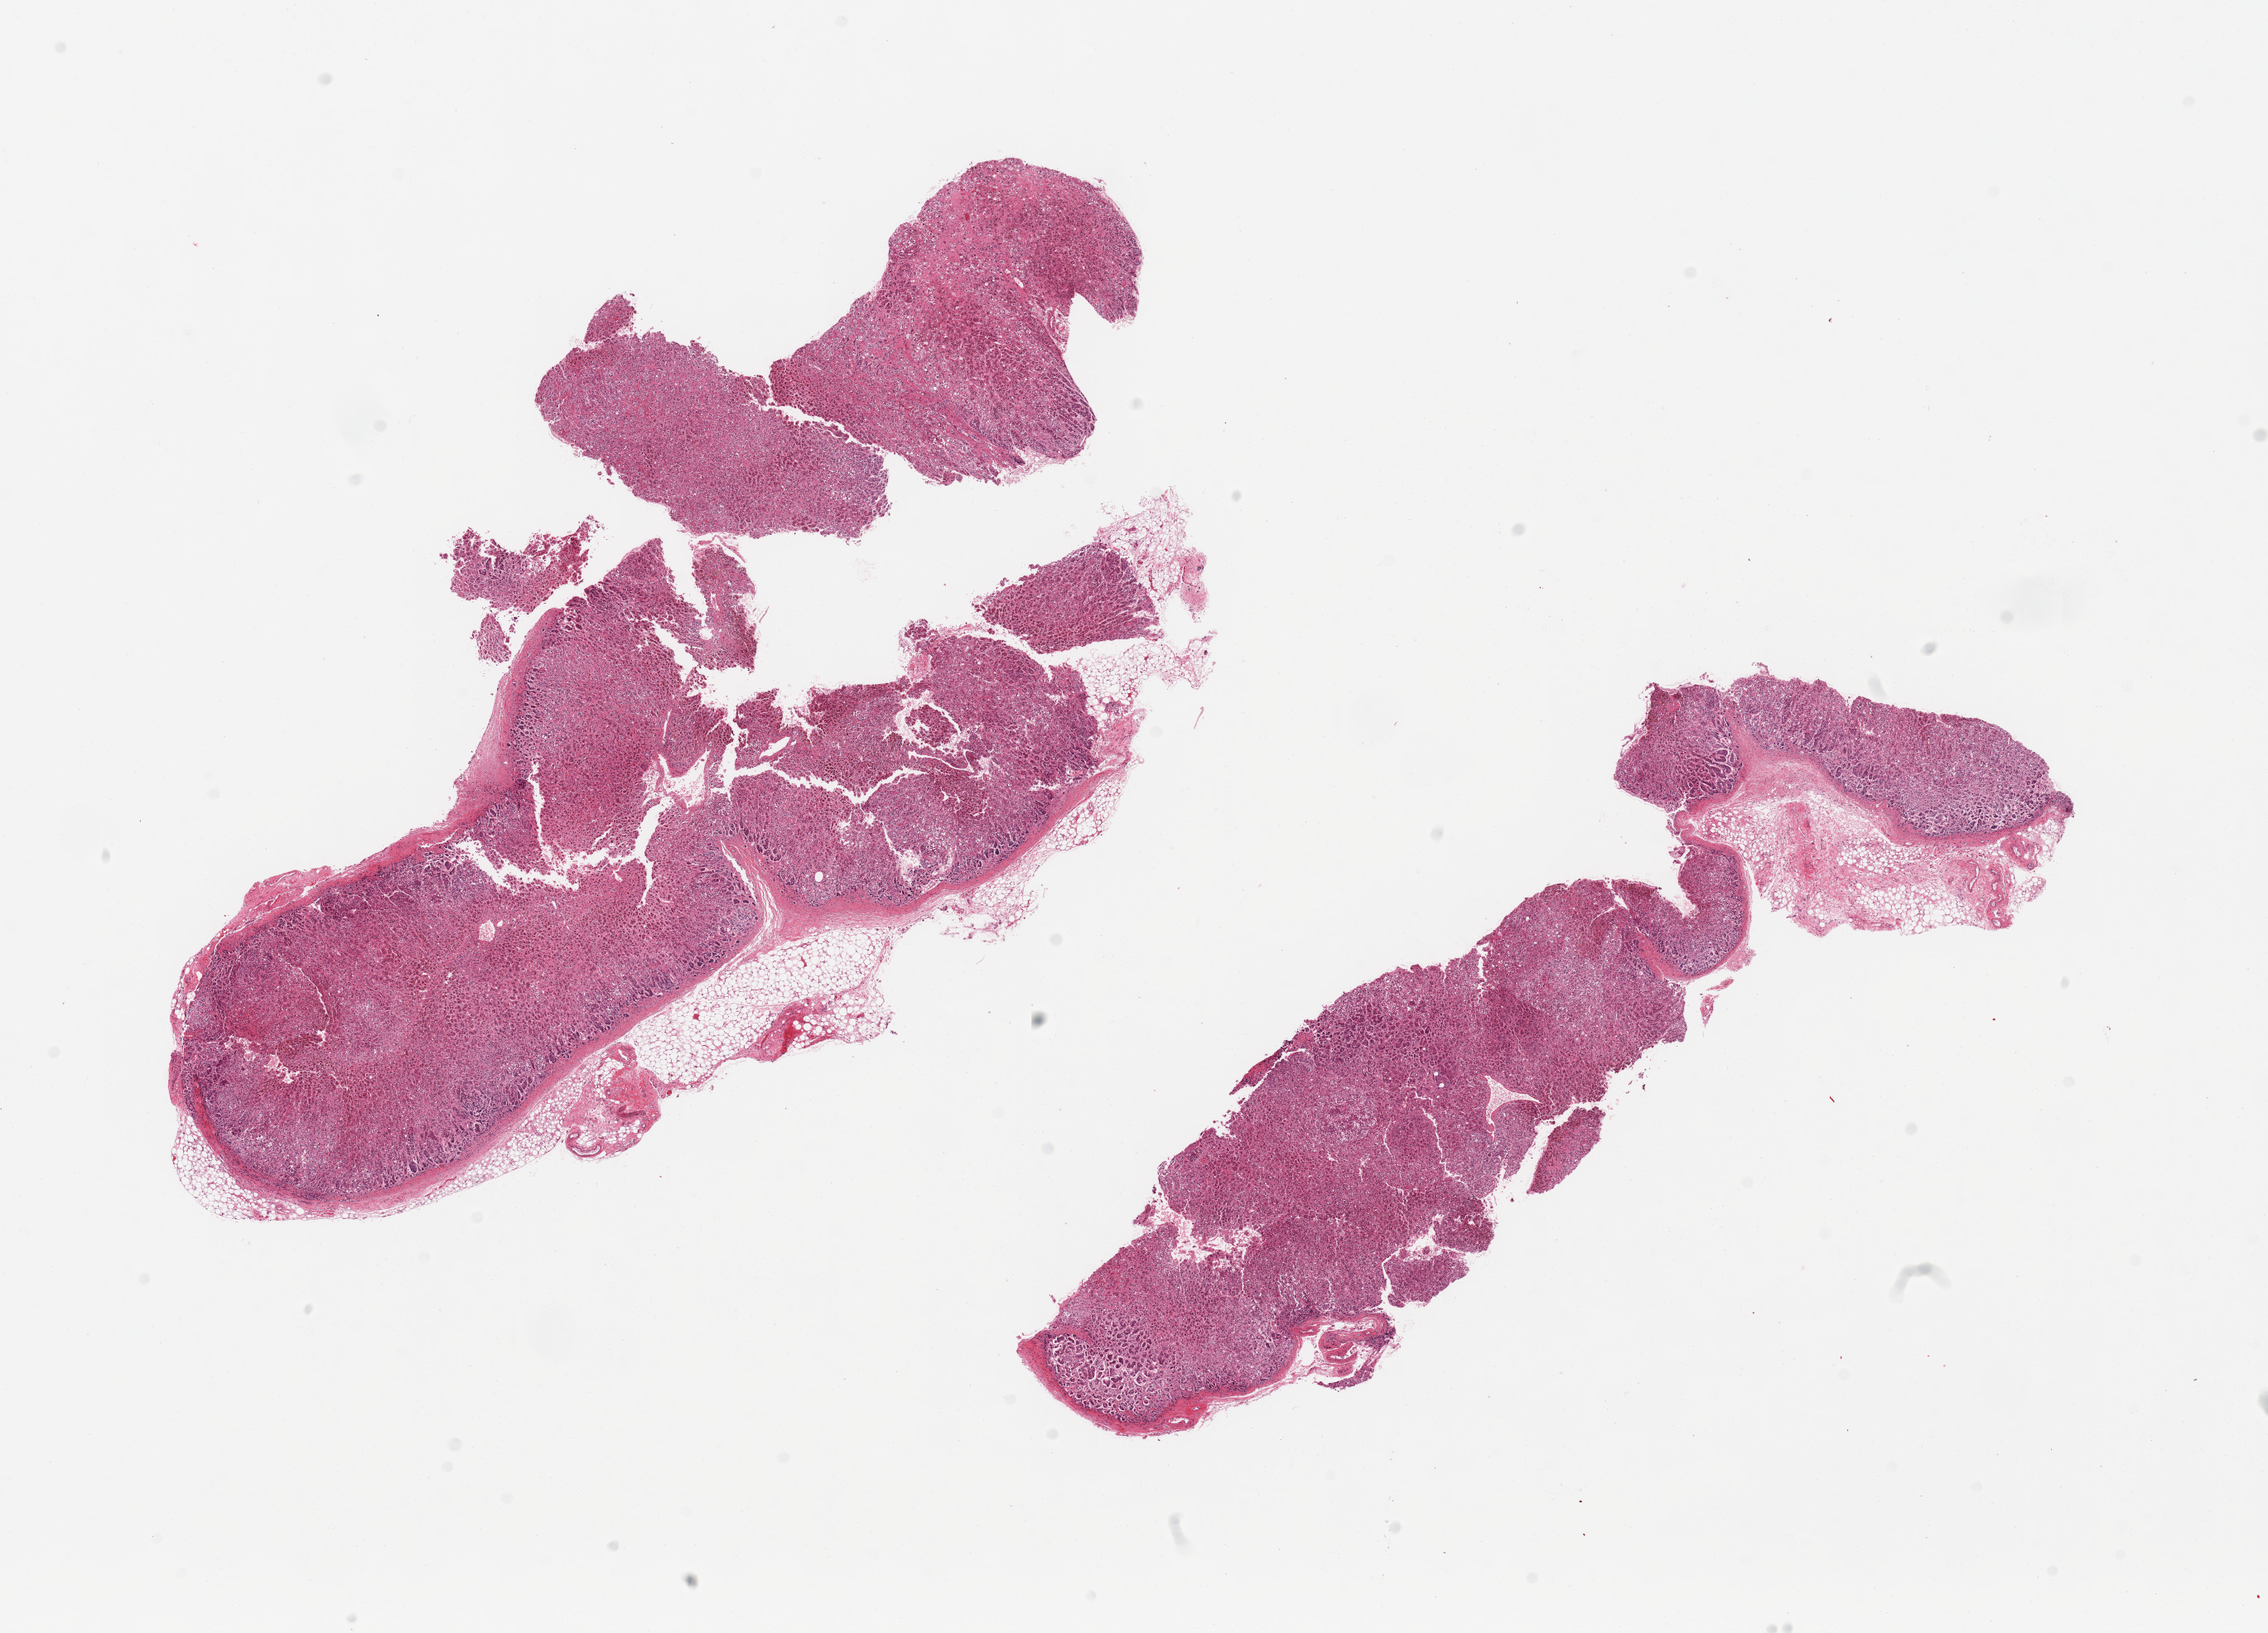
Haematoxylin and eosin whole-slide image — whole scanned area (about 21.7 x 15.6 mm) shown as a low-resolution overview. PAXgene-fixed, paraffin-embedded tissue. Section of adrenal gland (target tissue). Donor tissue sample. Donor: male.
- pathologist's review note for this sample: 2 pieces, cortex, ~10% adherent fat